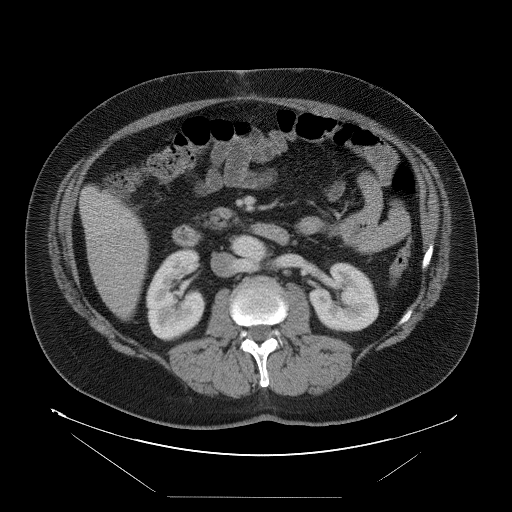
Contrast-enhanced abdominal CT, one axial slice. Position 29 of 114 along the scan axis. 120 kVp. Soft-tissue window (W 400 / L 40 HU). 5 mm slice thickness. 512 × 512 image matrix, field of view 500 × 500 mm. Male patient, age 61 years. From the clinical record (not read from this slice): diagnosis: colorectal cancer liver metastases, imaged before liver resection; multiple liver metastases: no; largest metastasis: 6.5 cm; disease in both lobes: yes.
Annotated regions visible in this slice (expert manual segmentation):
- liver: box from (x=81, y=187) to (x=149, y=319) px